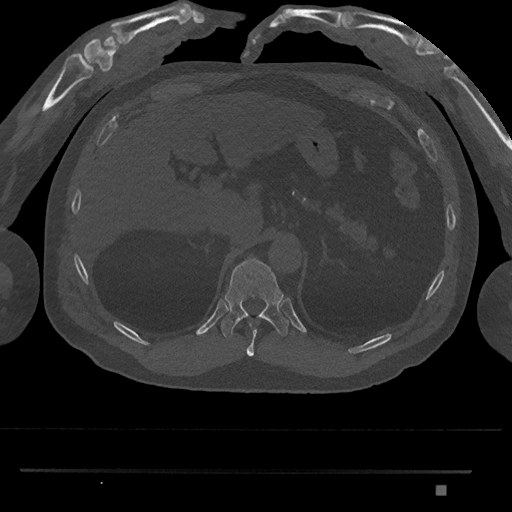
CT including the spine, one axial slice. Position 960 of 1134 along the scan axis. Bone window (W 1800 / L 400 HU). 0.5 mm slice thickness. 512 × 512 image matrix, field of view 429 × 429 mm. Patient: male, 65 years. Case-level facts recorded for this patient, not image findings: primary cancer: prostate.
Annotated regions visible in this slice (semi-automatically segmented with operator editing):
- T10 vertebra: box from (x=246, y=324) to (x=257, y=357) px
- T11 vertebra: (x=221, y=258)–(x=289, y=339)